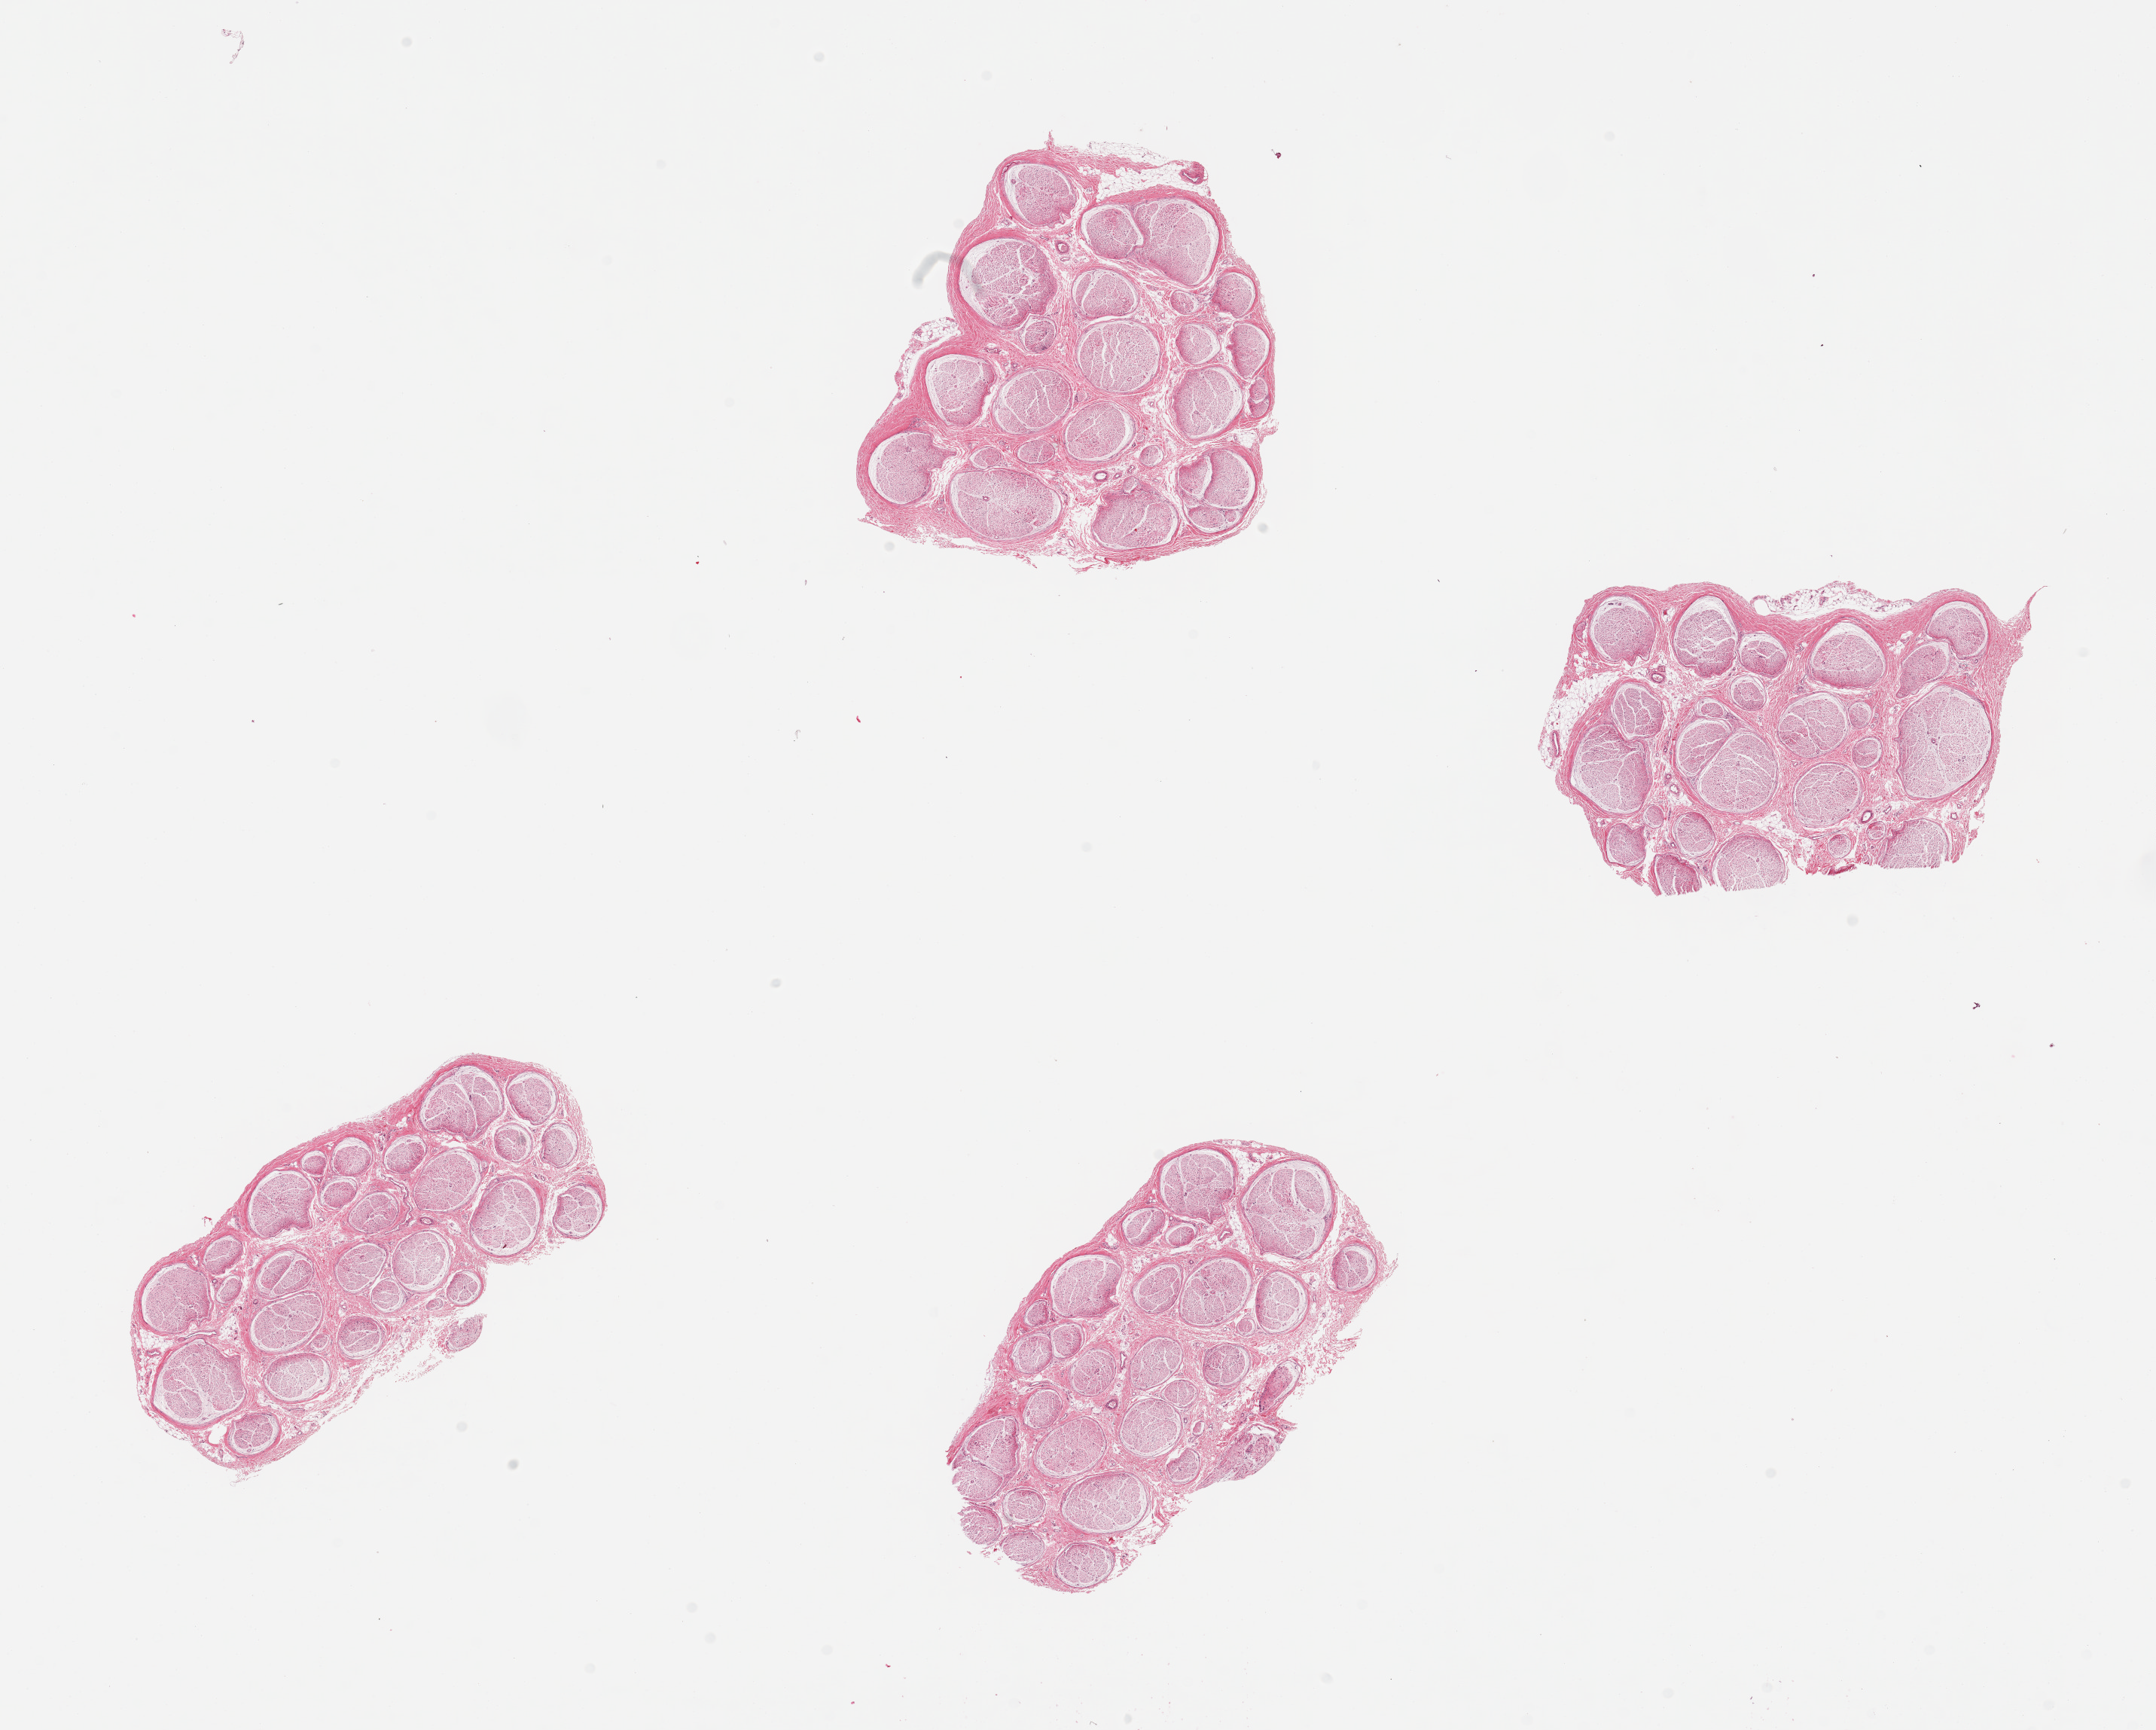
Whole-slide image, H&E stain, shown as a low-resolution overview of the whole scanned area (about 22.6 x 18.2 mm, slide scanned at 20x), PAXgene-fixed, paraffin-embedded tissue, section of tibial nerve (target tissue), donor tissue sample. Donor sex: female.
* pathologist's review note for this sample: 4 pieces, clean specimens, minimal fat